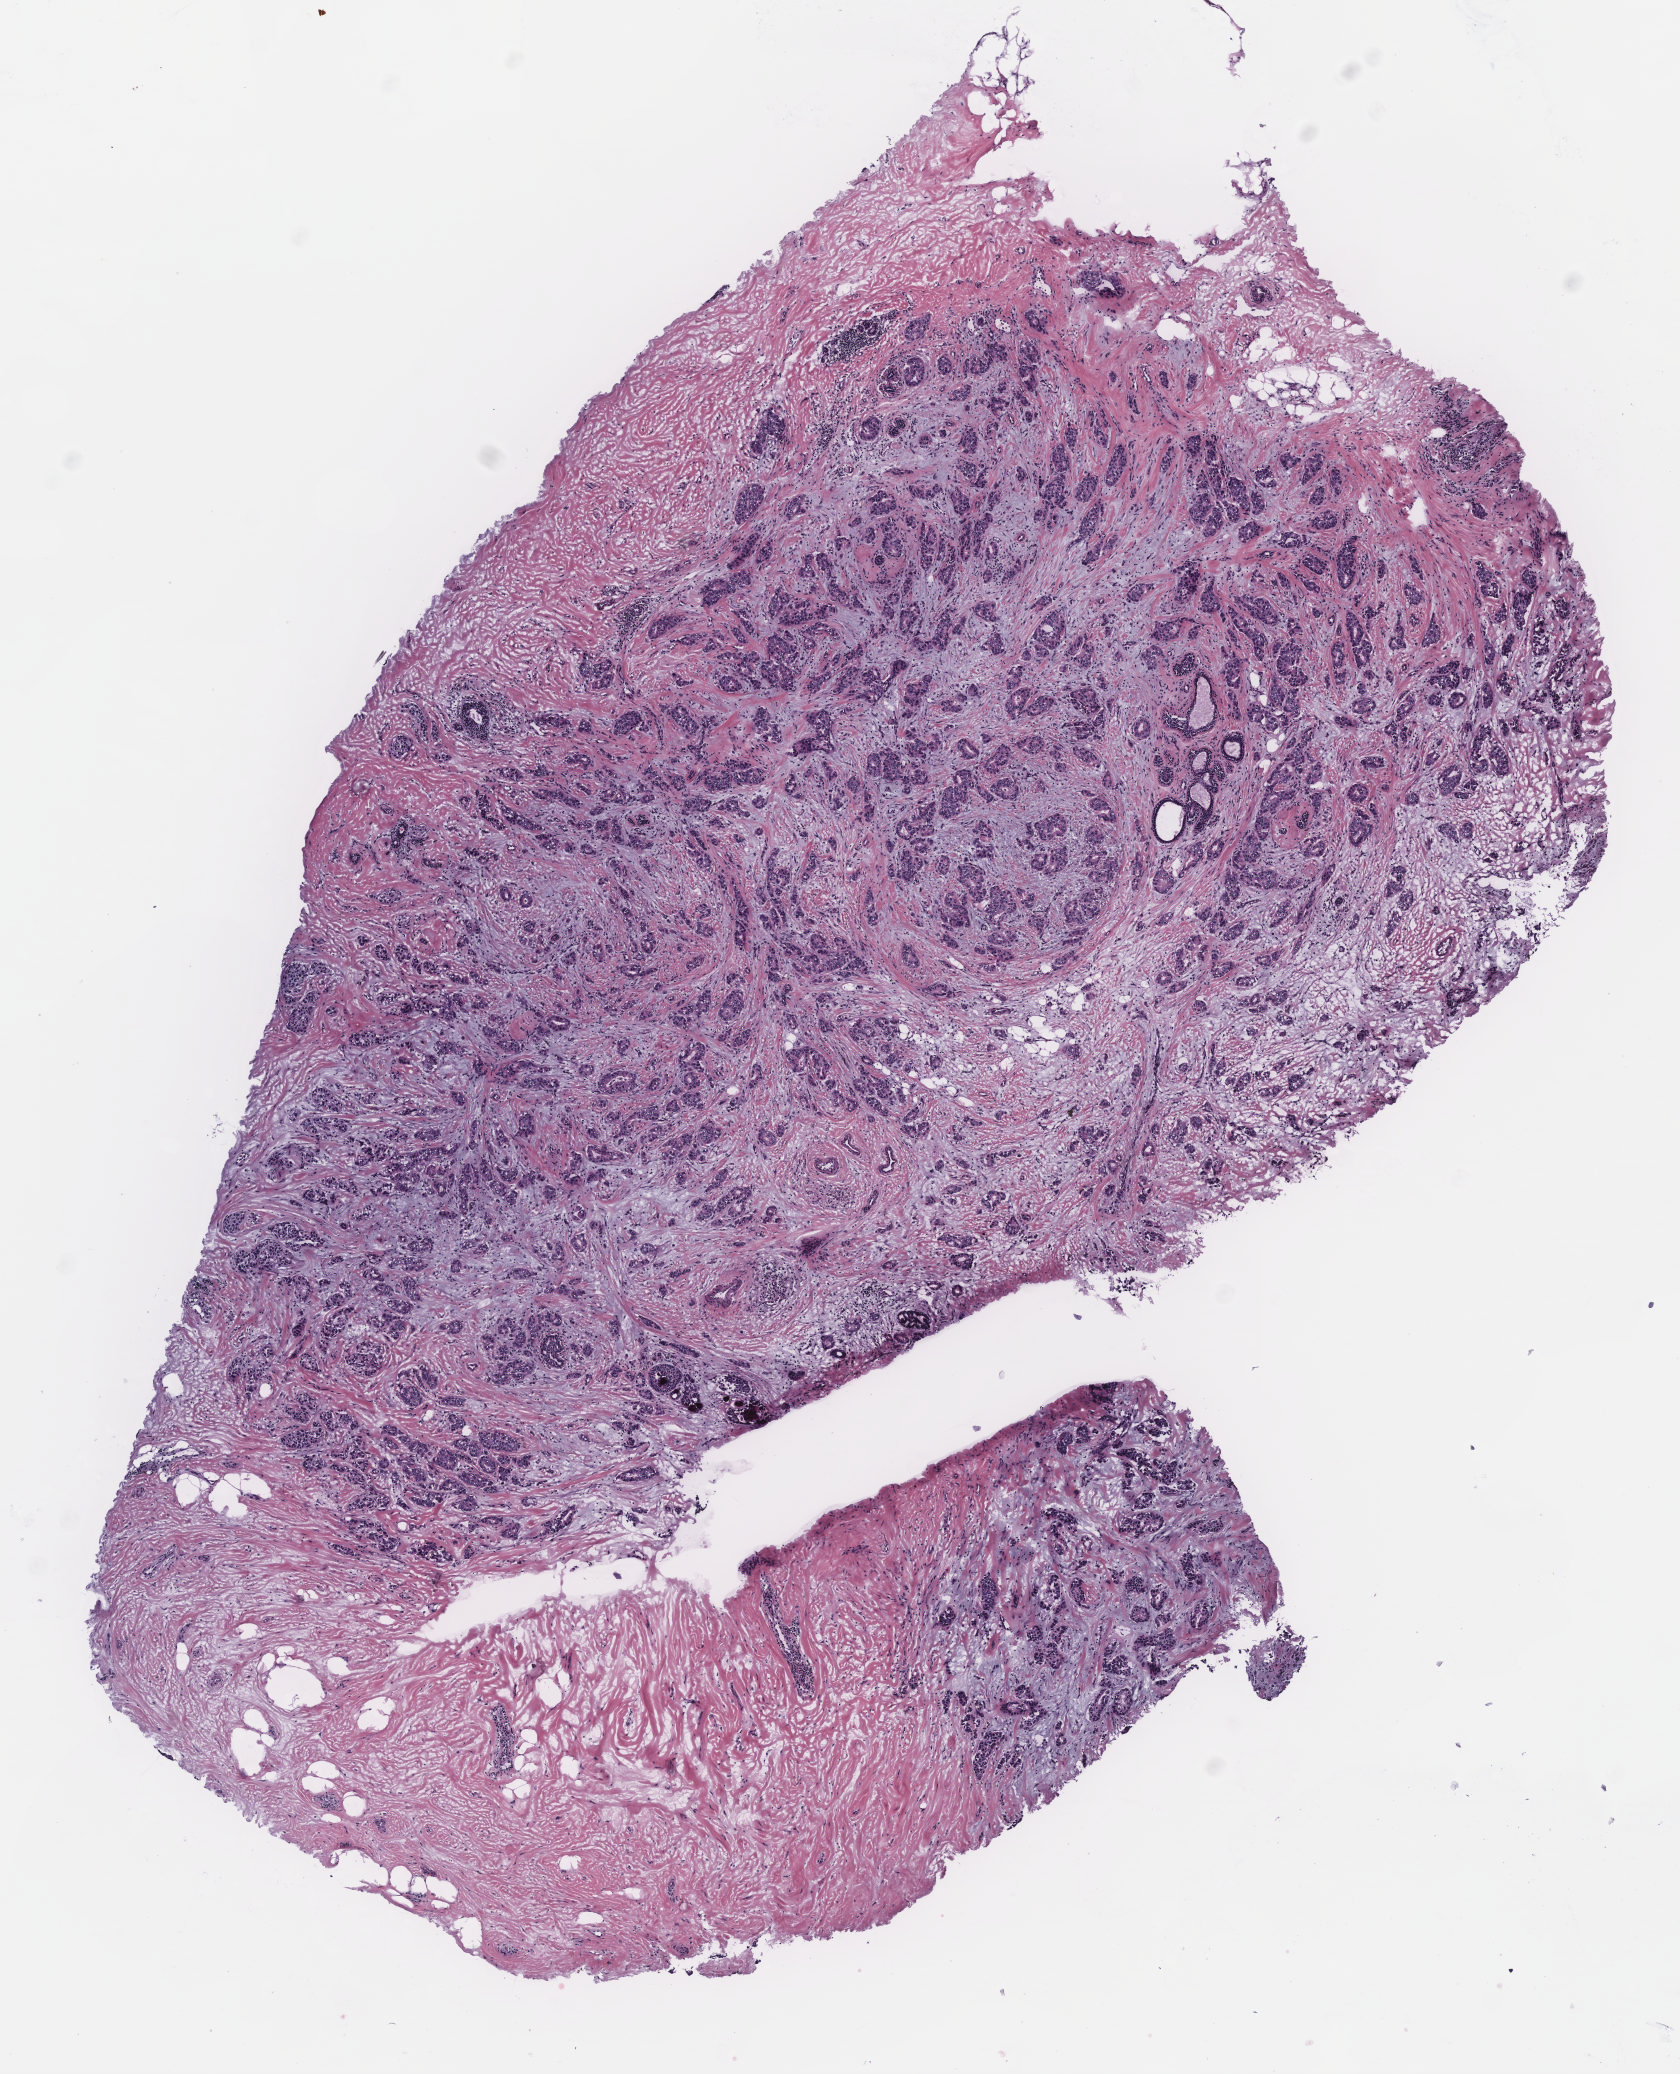
Digitized H&E-stained tissue section (whole slide), whole scanned area (about 6.7 x 8.3 mm, from a 40x scan) shown as a low-resolution overview; breast, tumour tissue. Female, 60 y/o.
• AJCC pathologic stage: IIIA
• histologic diagnosis: Infiltrating duct carcinoma, NOS